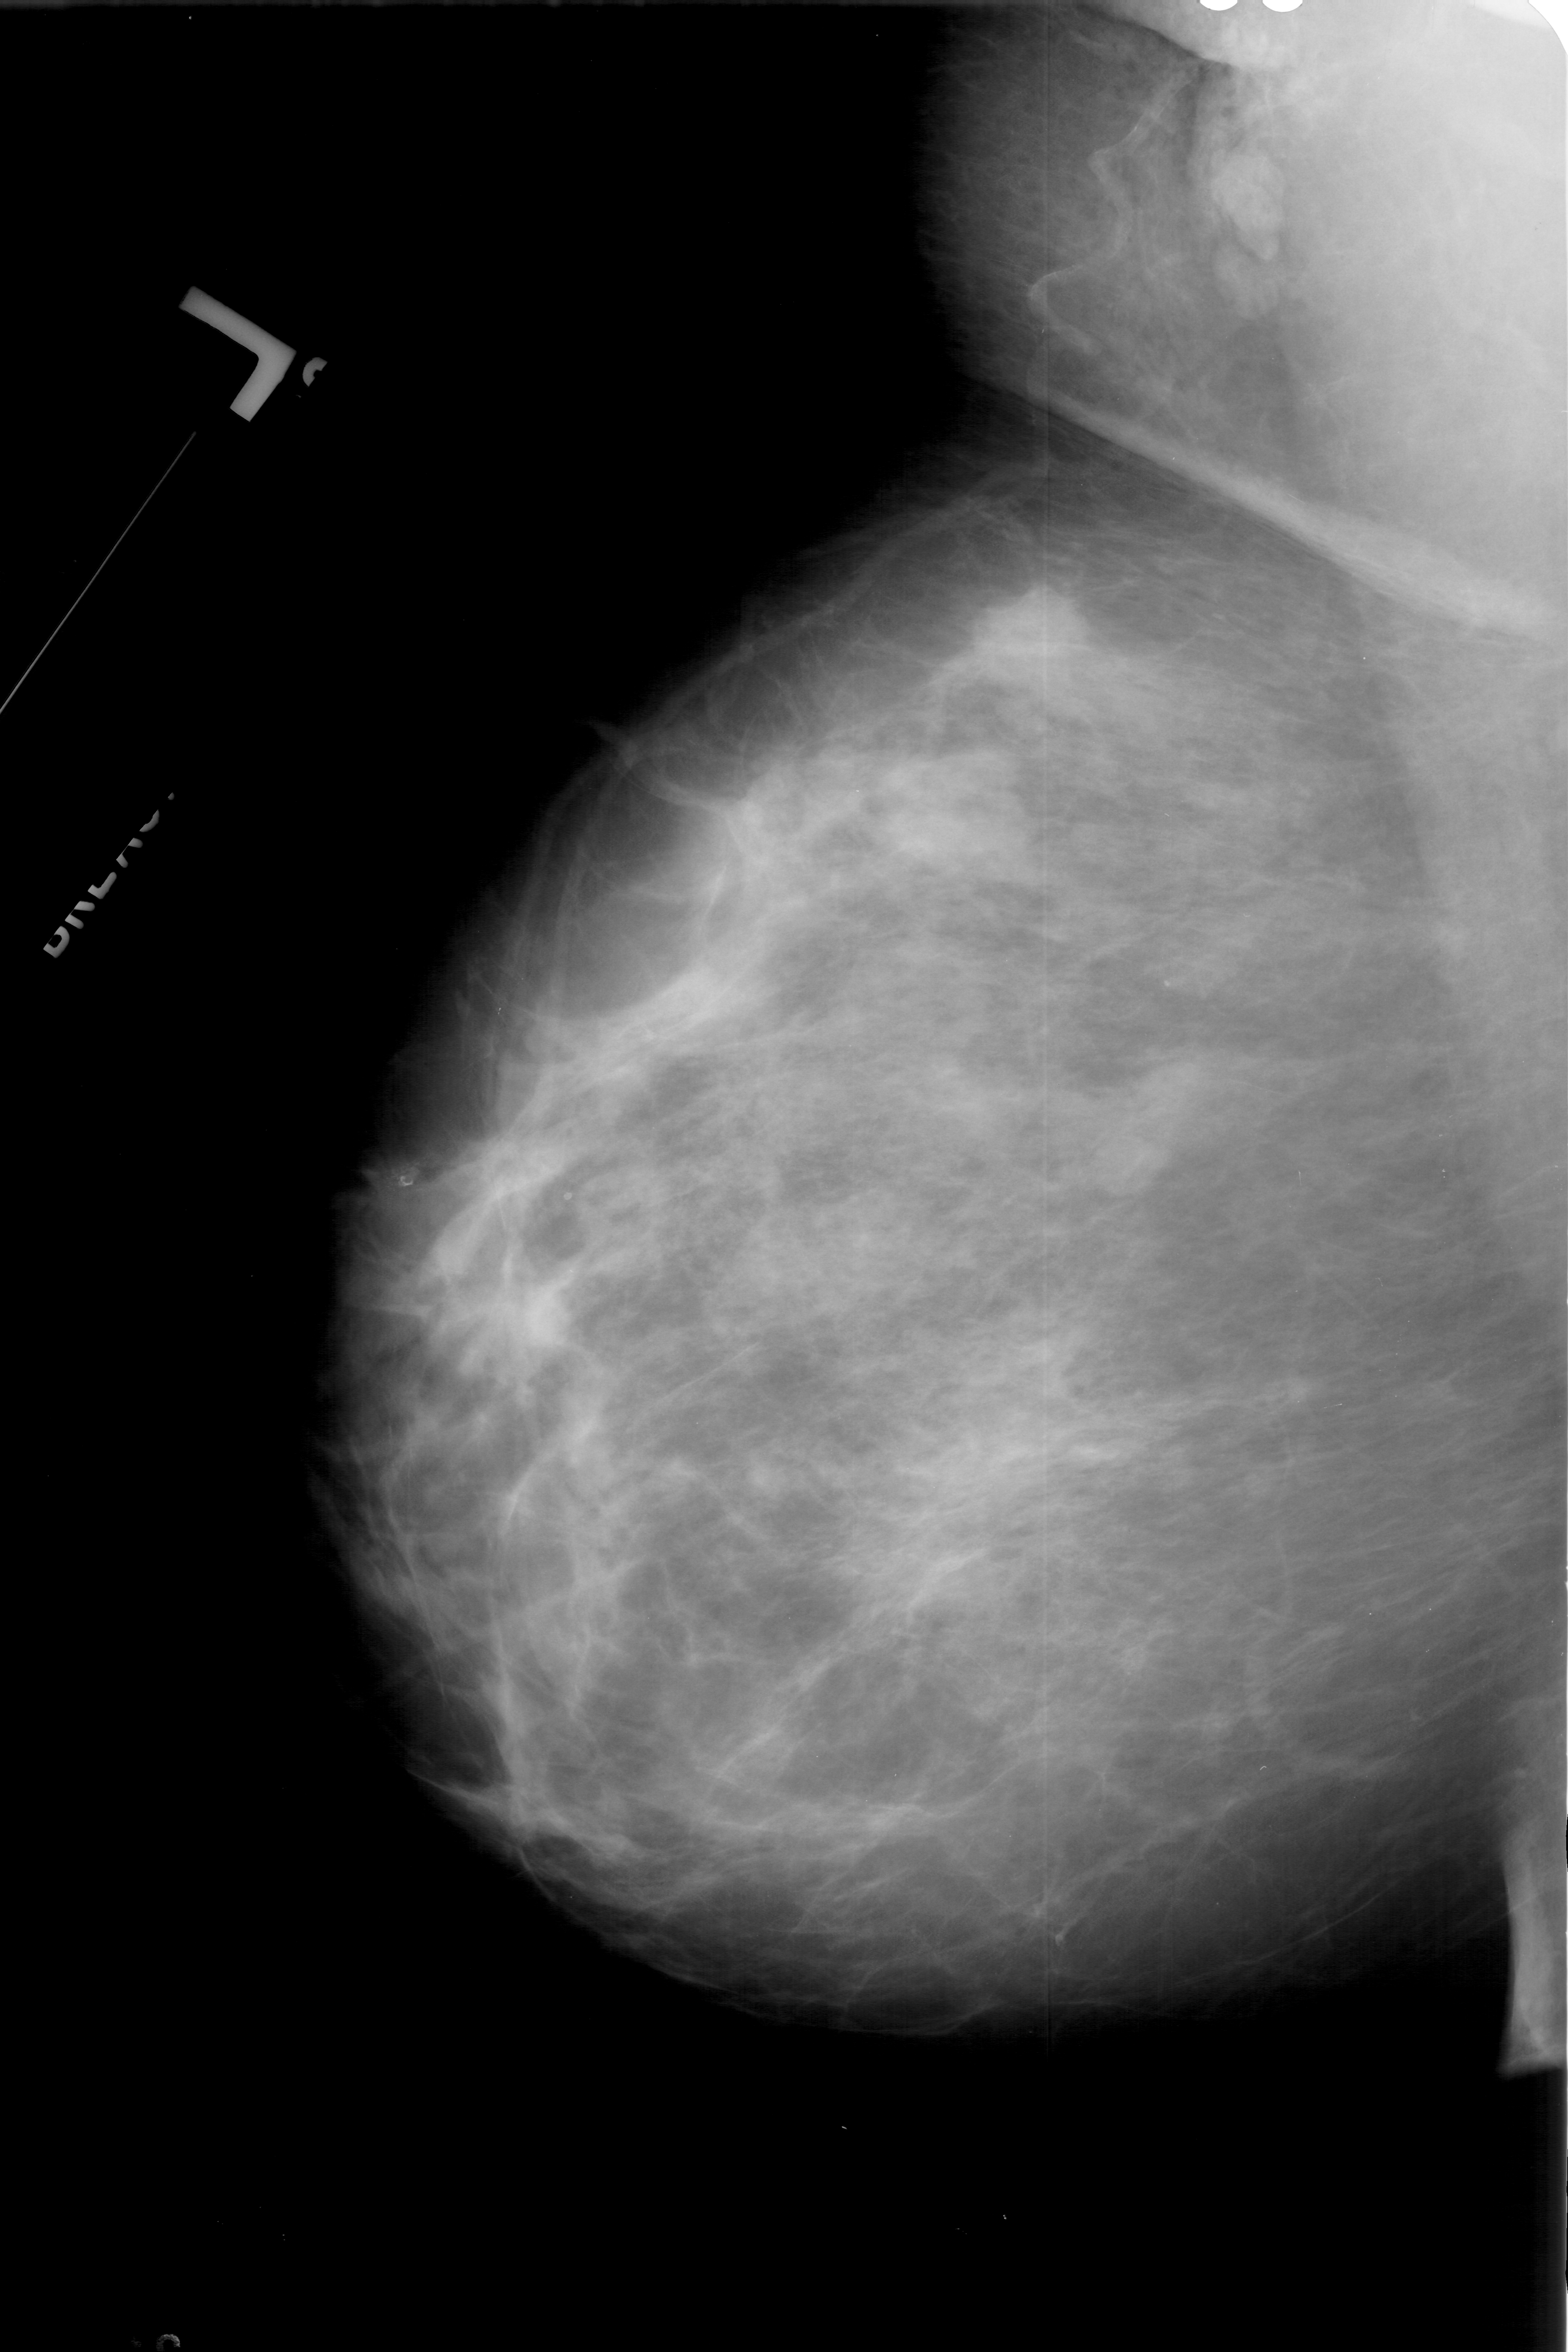
Digitized screen-film mammogram; left breast; mediolateral oblique (MLO) view; breast composition: heterogeneously dense (BI-RADS density category 3 of 4).
- Marked findings (only marked abnormalities are described; nothing is implied about the rest of the image): mass, shape lobulated, margins ill defined; BI-RADS assessment category 4; pathology result (as recorded, not read from the image): malignant.